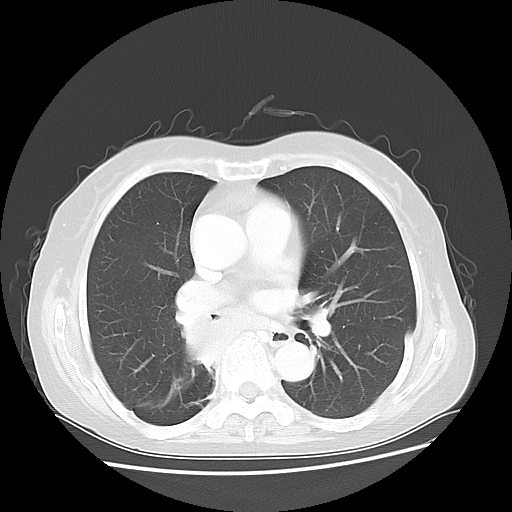
Chest CT, one axial slice; reconstruction kernel LUNG; lung window (W 1500 / L -600 HU); 5 mm slice thickness; 512 × 512 image matrix, field of view 360 × 360 mm. Female patient, age 63 years. From the clinical record (not read from this slice): clinical TNM (as recorded): T2 N3 M1b.
Outlined on this slice (rectangle marked by the reading radiologist):
- lung tumour (recorded histology: small cell carcinoma): bounding box <172,309,228,388> (left, top, right, bottom; pixels)